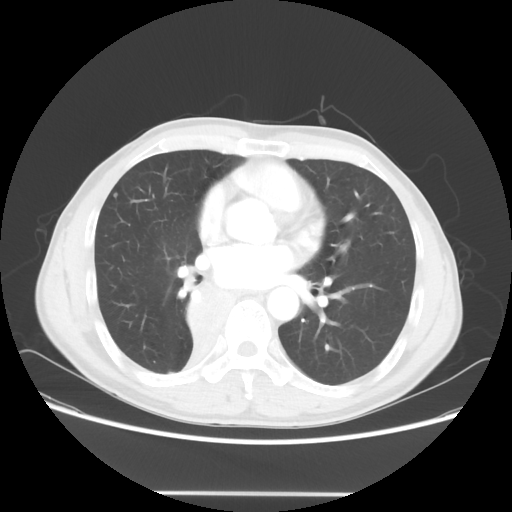
Chest CT, one axial slice; slice 30 of 62 in the series (ordered by position); reconstruction kernel STANDARD; 120 kVp; lung window (W 1500 / L -600 HU); 5 mm slice thickness; 512 × 512 image matrix, field of view 393 × 393 mm. Patient: male, 47 years. From the clinical record (not read from this slice): clinical TNM (as recorded): T2 N0 M0.
Structures marked on this image (bounding box drawn by a radiologist):
- lung tumour (recorded histology: squamous cell carcinoma): box from (x=178, y=276) to (x=228, y=366) px